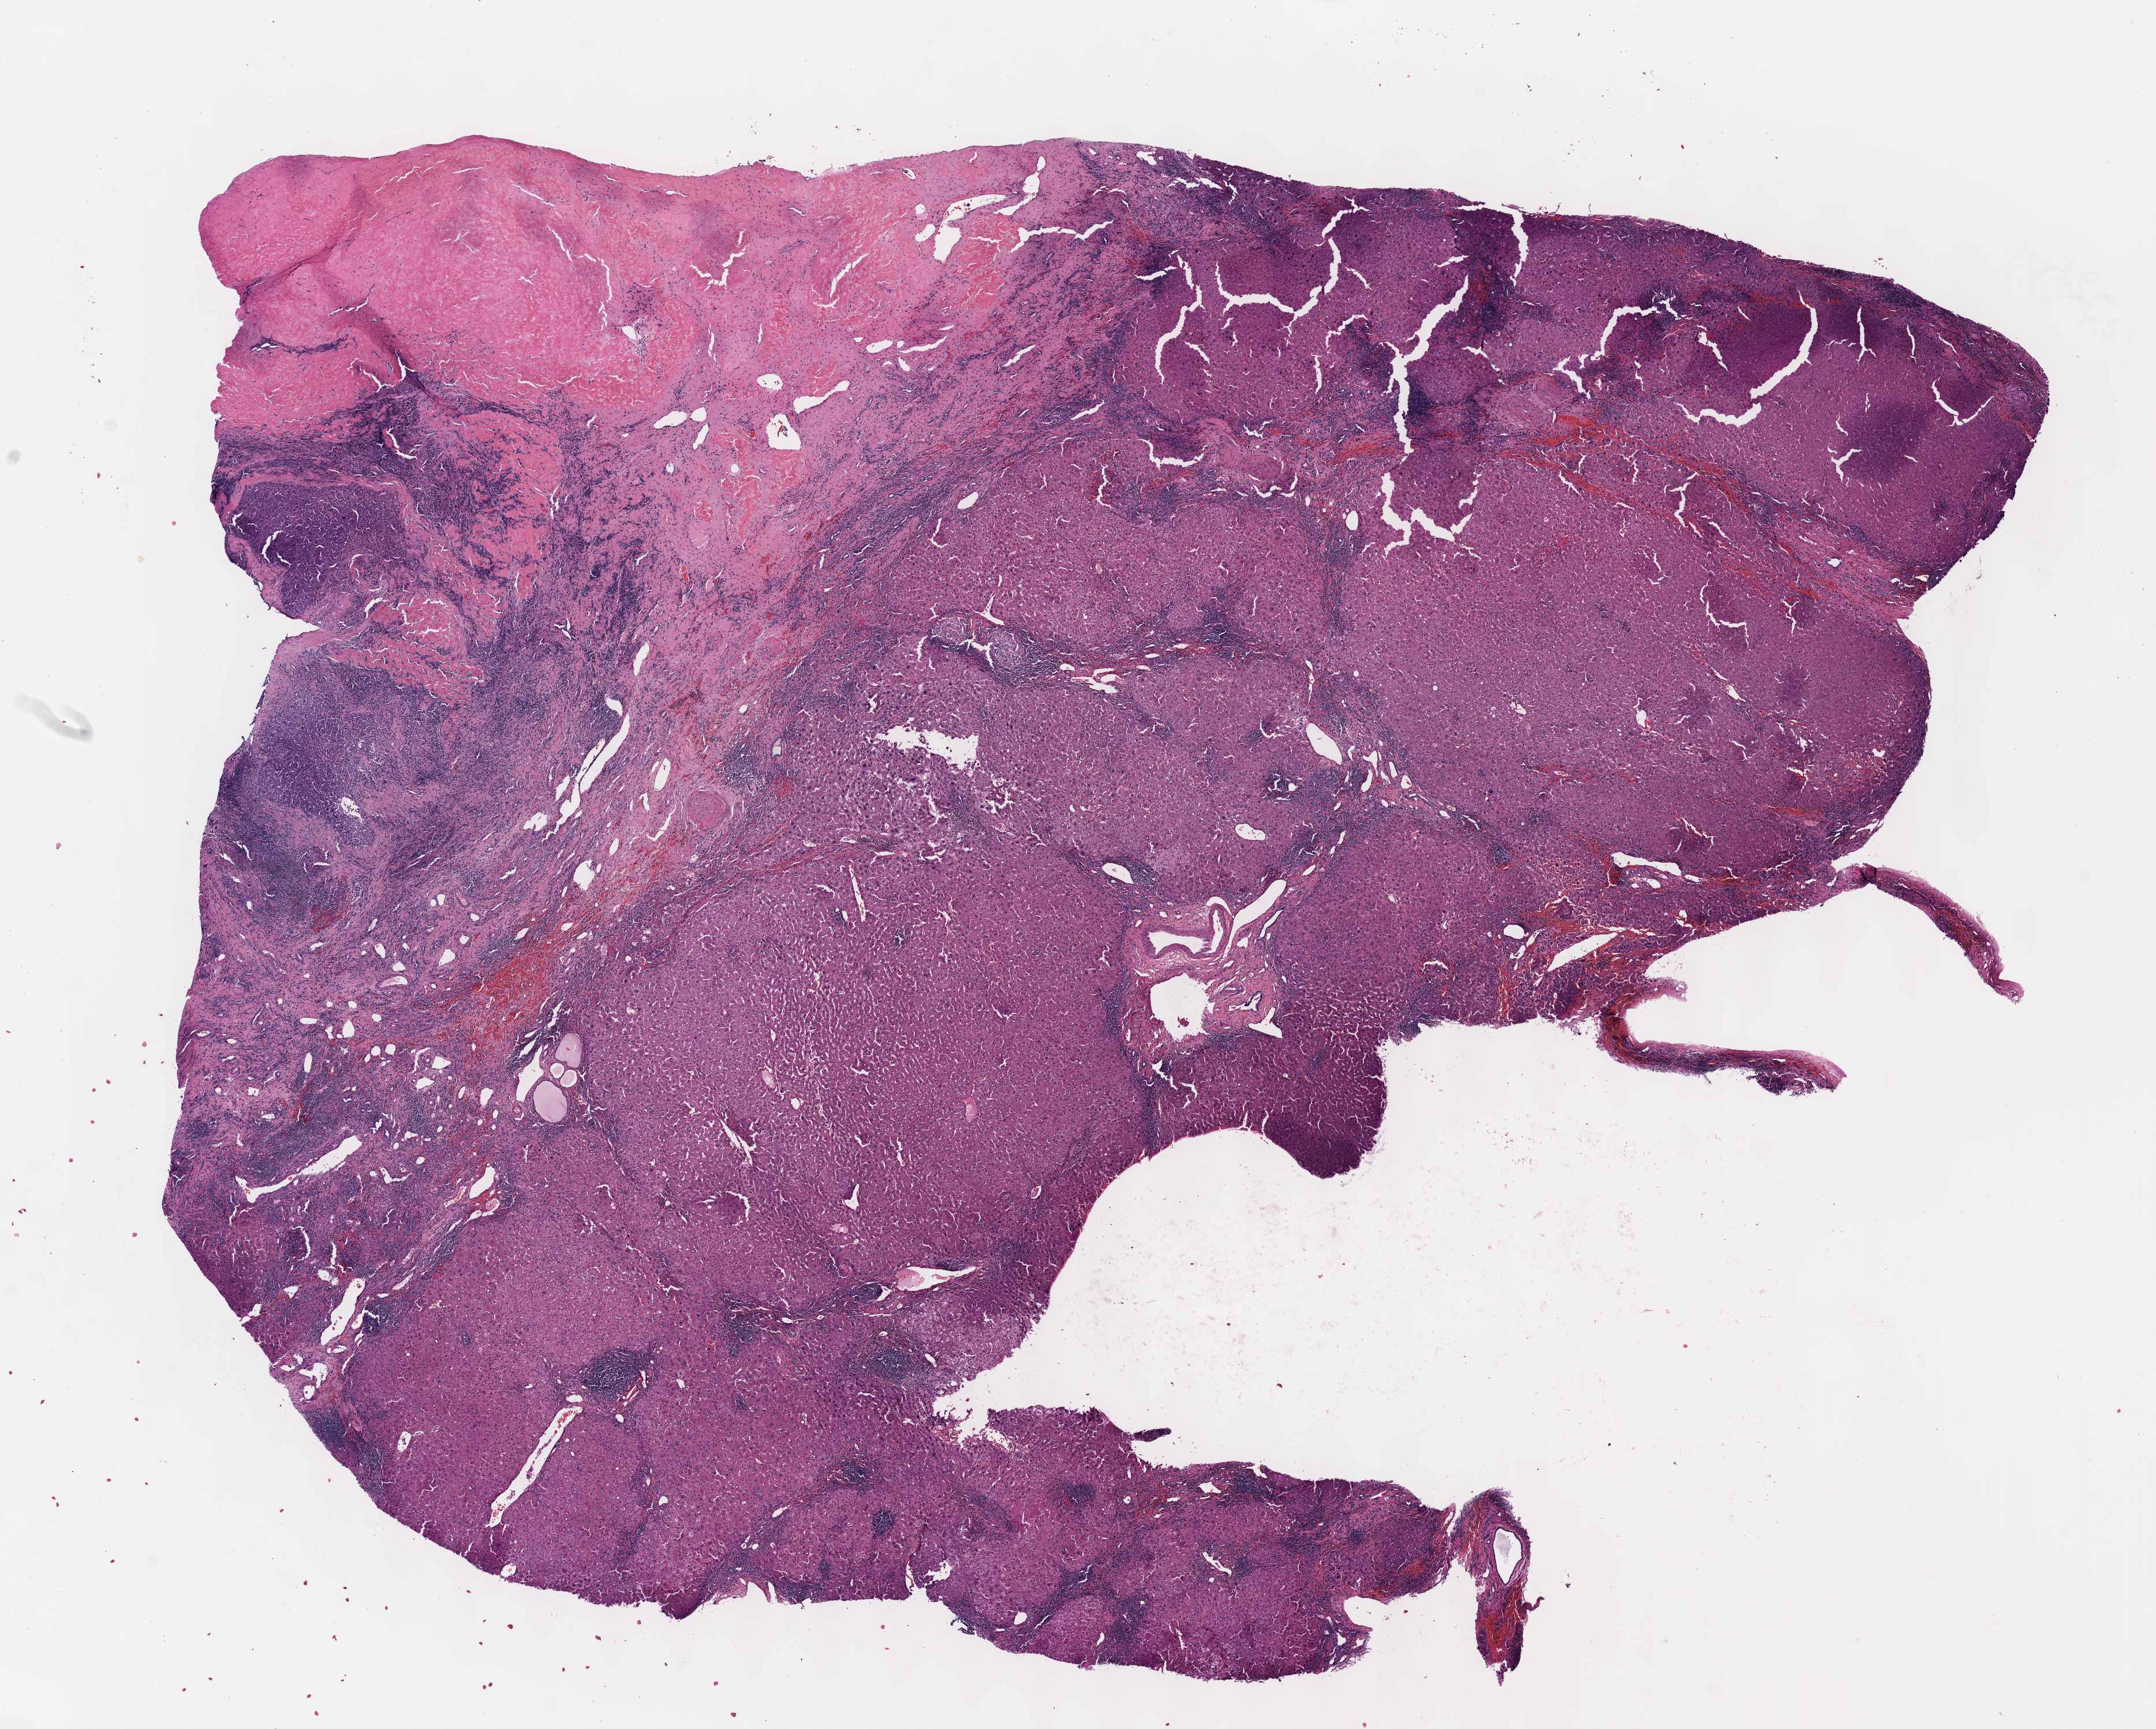
Digitized H&E tissue section (whole slide) — low-resolution overview of the scanned area, about 15.1 x 12.1 mm, formalin-fixed paraffin-embedded (FFPE) diagnostic section, liver, primary tumour sample. Male, age 61 years at initial diagnosis.
Diagnosis: Combined hepatocellular carcinoma and cholangiocarcinoma.